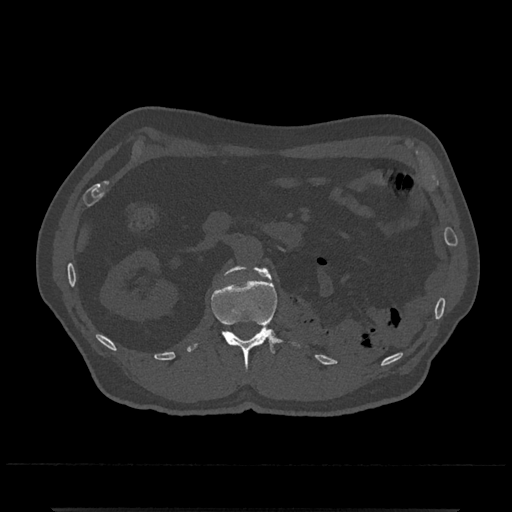
CT including the spine, one axial slice. Slice 353 of 797 in the series (ordered by position). 120 kVp. Bone window (W 1800 / L 400 HU). 0.5 mm slice thickness. 512 × 512 image matrix, field of view 393 × 393 mm. Patient: male, 67 years. From the clinical record (not read from this slice): primary cancer: prostate.
Structures marked on this image (semi-automatic segmentation, software-assisted and operator-edited):
- L1 vertebra: box from (x=188, y=266) to (x=300, y=371) px